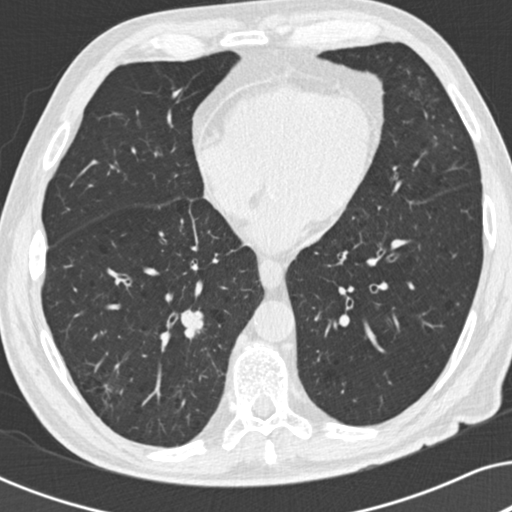
Chest CT (low-dose screening protocol), one axial image. Baseline annual screen. Lung window (W 1500 / L -600 HU). Standard (soft-tissue) reconstruction kernel (B30f). 512 × 512 image matrix. Male, age 73 years at enrolment. Current smoker at enrolment.
• Lesion marked by an expert reader, bounding box [x1, y1, x2, y2] px = [163, 299, 225, 359].
• The screening reader recorded 2 non-calcified nodules or masses ≥4 mm on this exam (right lower lobe, right upper lobe); which of them this box marks is not recorded.
• Participant outcome: lung cancer diagnosed 63 days after this screen — carcinoid tumor, NOS, right lower lobe, carcinoid, stage not assessed, 12 mm at pathology.